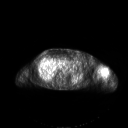
FDG PET of an extremity soft-tissue mass (from a PET/CT study), one axial slice; slice 139 of 267 in the series (ordered by position); 128 × 128 image matrix, field of view 700 × 700 mm. Patient: female, 83 years. Case-level facts recorded for this patient, not image findings: histological type: pleiomorphic leiomyosarcoma; grade: high; site of the primary tumour: left biceps.
Outlined on this slice (expert contour drawn on MRI and transferred to this co-registered scan by the dataset authors):
- gross tumour volume including surrounding oedema: bounding box [x1, y1, x2, y2] px = [103, 70, 107, 75]